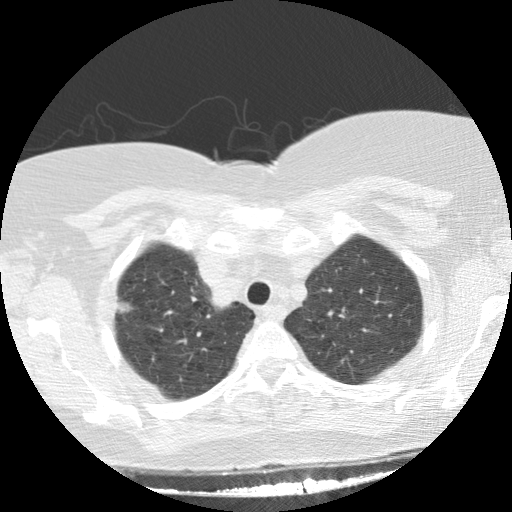
Low-dose screening chest CT, one axial slice. Slice 115 of 136 in the series (ordered by position). Reconstruction kernel STANDARD. 120 kVp. Lung window (W 1500 / L -600 HU). 2.5 mm slice thickness. 512 × 512 image matrix, field of view 330 × 330 mm.
Outlined on this slice (outlined manually by an expert reader):
- lesion 1 (tumor, upper lobe of right lung): box from (x=118, y=302) to (x=133, y=314) px